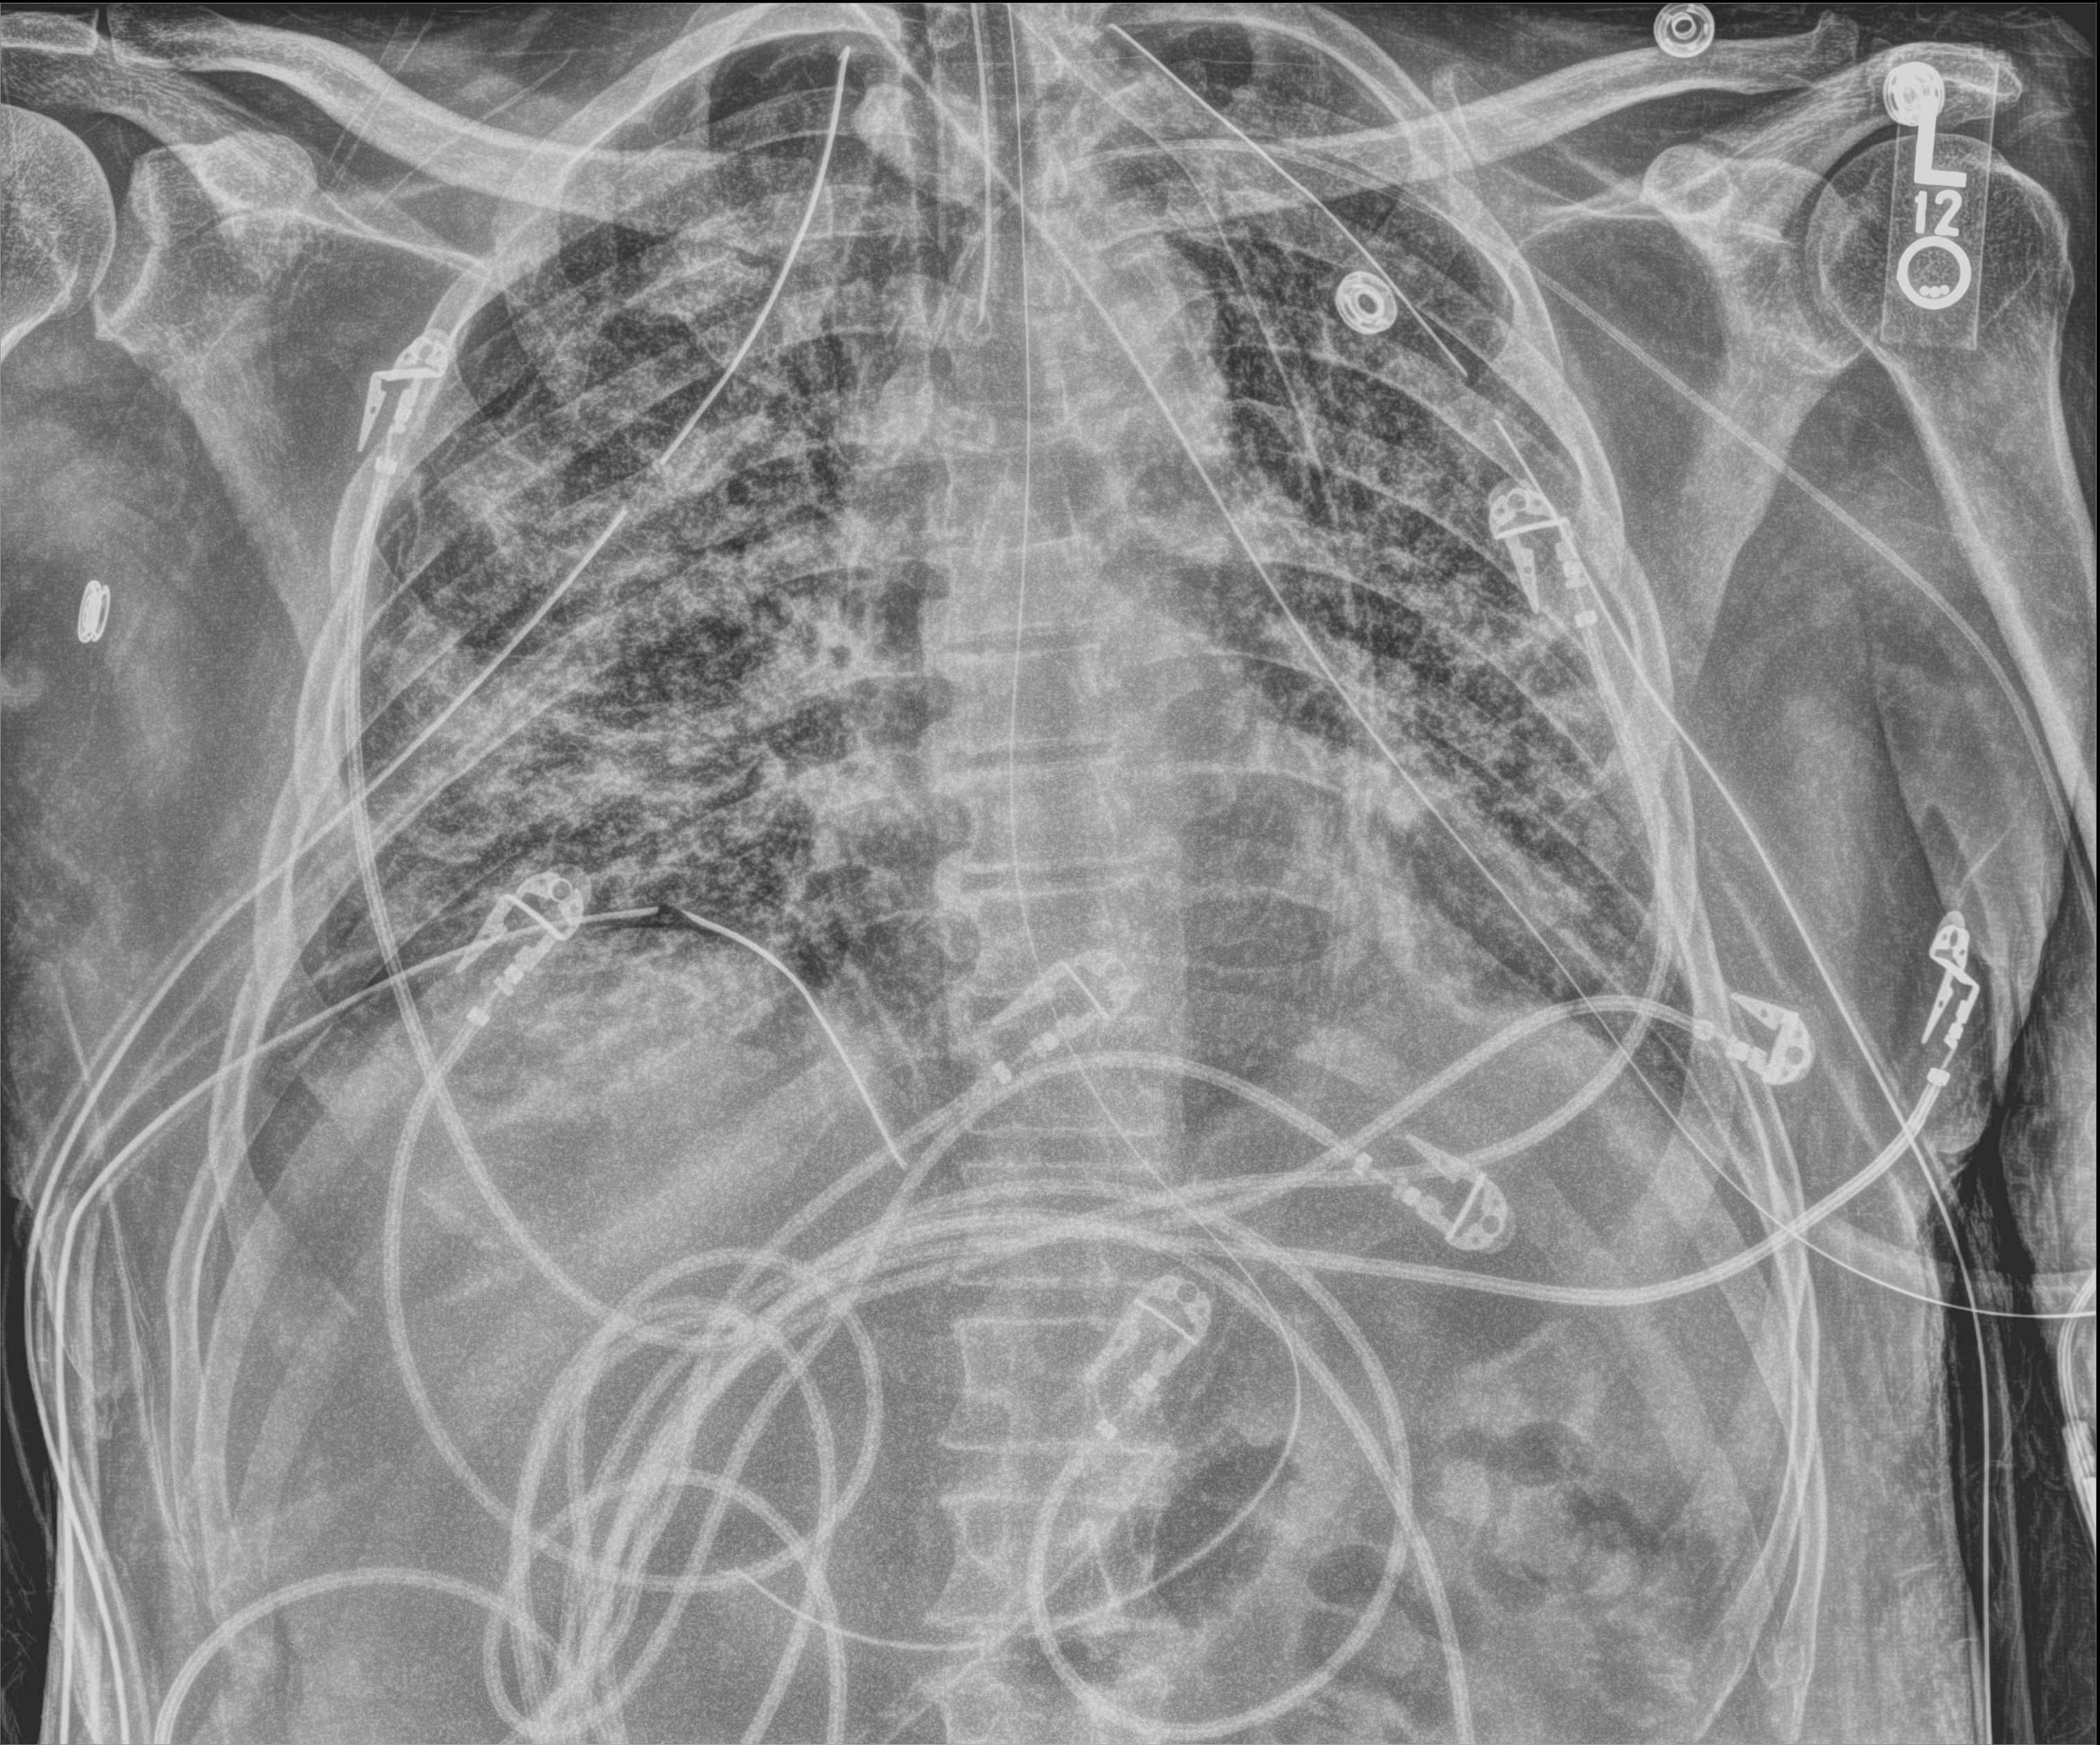
Chest X-ray (portable), anteroposterior (AP) projection. Patient hospitalised with COVID-19; male, aged 18–59 years.
Hospital-stay facts (about this admission, not read from this image; timing relative to this image not recorded): mechanically ventilated during this hospital stay: yes; admitted to intensive care during this hospital stay: yes.